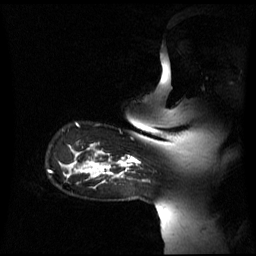
Breast MRI (dynamic contrast-enhanced), one sagittal slice. Position 50 of 60 along the scan axis. Dynamic contrast-enhanced series, image 2 of 3 at this slice position (ordered by acquisition). 1.5 T. TE 4.2 ms, TR 8.4 ms. 256 × 256 image matrix, field of view 270 × 270 mm. Patient: female, 39 years. From the clinical record (not read from this slice): setting: breast cancer imaged before/during neoadjuvant chemotherapy; receptor status: triple-negative.
Outlined on this slice (semi-automatic segmentation, software-assisted and operator-edited):
- analysis volume of interest (the breast-tissue region the enhancement analysis was run in; not a lesion): bounding box <105,157,139,176> (left, top, right, bottom; pixels)
- tumour enhancement mask (voxels above the 70 % enhancement threshold inside the analysis volume of interest): <105,157,139,175>